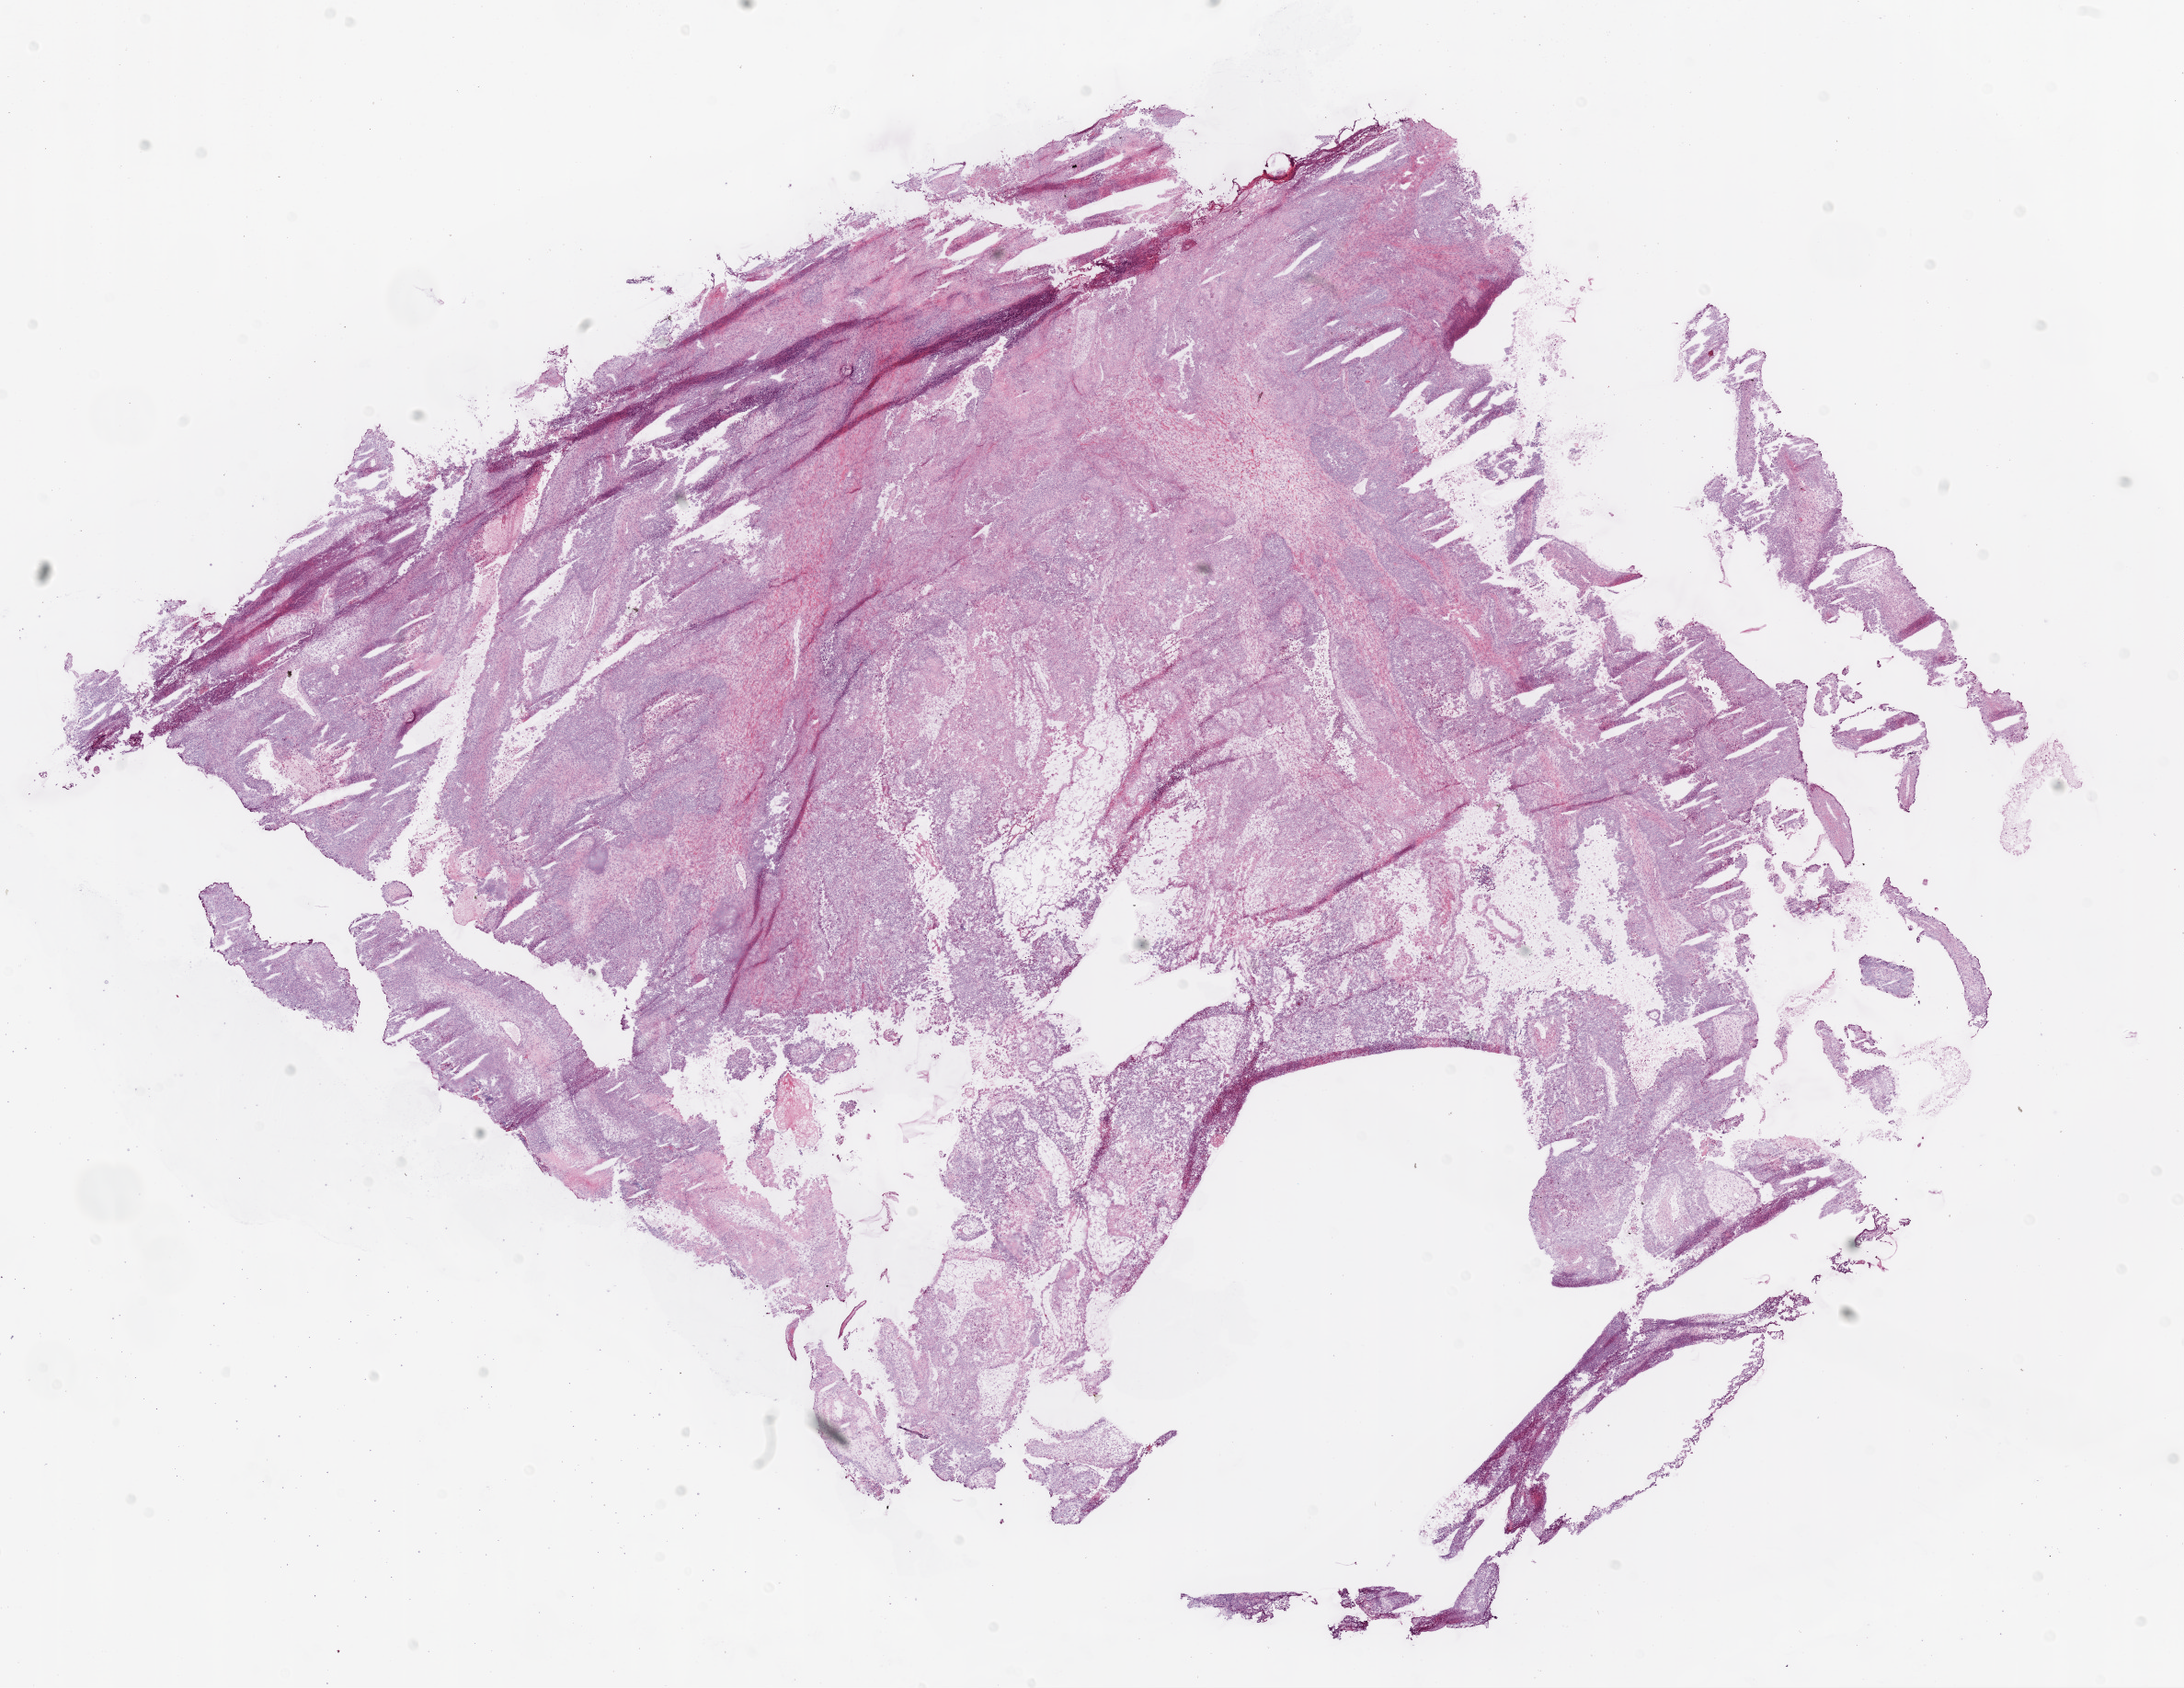
Digitized H&E tissue section (whole slide) — a low-resolution overview of the entire scanned area, about 19.1 x 14.7 mm. Frozen section from the bottom of the tissue portion. Primary tumour sample from the ovary. Patient: female, age at initial diagnosis 82 years. Histologic grade: G3 (poorly differentiated). Pathologist review of this section (percent, as recorded): tumour cells 78%, tumour nuclei 90%, normal cells 0%, stromal cells 20%, necrosis 2%.
Diagnosis: Serous cystadenocarcinoma, NOS. FIGO stage: IIIC.